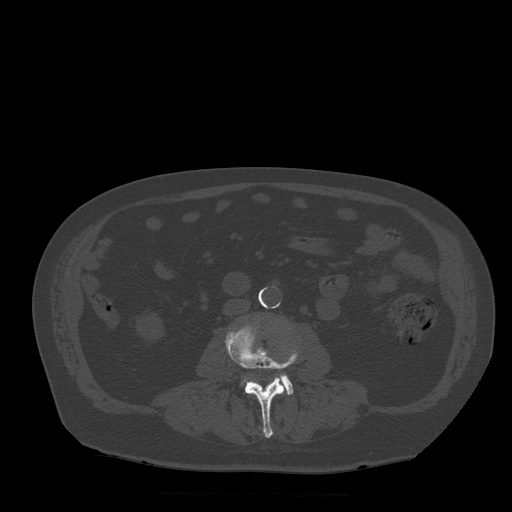
CT including the spine, one axial slice; bone window (W 1800 / L 400 HU); 512 × 512 image matrix. Patient age 72 years. From the clinical record (not read from this slice): primary cancer: prostate.
Structures marked on this image (semi-automatically segmented with operator editing):
- L3 vertebra: bounding box [x1, y1, x2, y2] px = [225, 323, 299, 438]
- L4 vertebra: [243, 375, 294, 395]